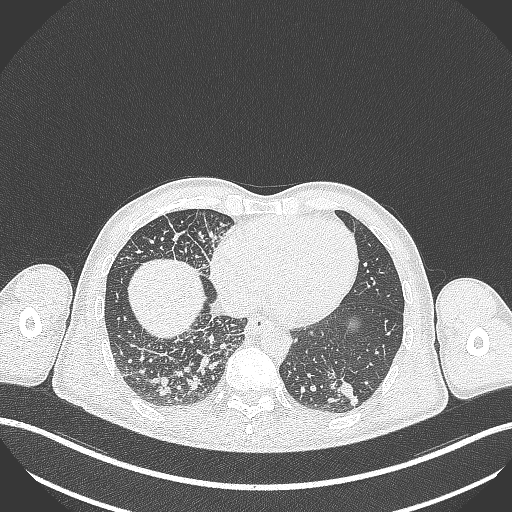
Chest CT, one axial slice. Reconstruction kernel B70f. Lung window (W 1500 / L -600 HU). 1 mm slice thickness. 512 × 512 image matrix, field of view 400 × 400 mm. Patient: male, 49 years. From the clinical record (not read from this slice): clinical TNM (as recorded): T2b N1 M0.
Annotated regions visible in this slice (bounding box drawn by a radiologist):
- lung tumour (recorded histology: adenocarcinoma): bounding box (x1, y1, x2, y2) in pixels: (323, 366, 365, 410)